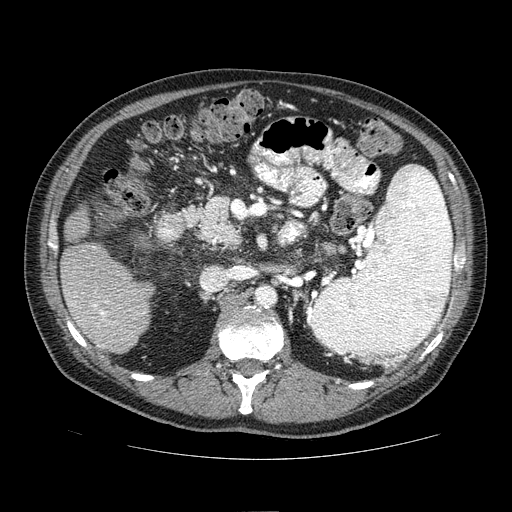
Contrast-enhanced abdominal CT (liver protocol), one axial slice. Slice 27 of 81 in the series (ordered by position). Reconstruction kernel STANDARD. One of 2 acquisitions stored at this slice position. Soft-tissue window (W 400 / L 40 HU). 512 × 512 image matrix. Case-level facts recorded for this patient, not image findings: diagnosis: hepatocellular carcinoma (patient treated with transarterial chemoembolisation; whether this scan precedes or follows treatment is not stated here); TNM stage (as recorded): Stage-IIIA; Child-Pugh class: A.
Outlined on this slice (semi-automatic segmentation, software-assisted and operator-edited):
- liver parenchyma outside the tumour (the mass and vessels are separate outlines, so this box may not span the whole liver): box from (x=60, y=208) to (x=154, y=353) px
- liver vessels: (x=72, y=246)–(x=115, y=346)